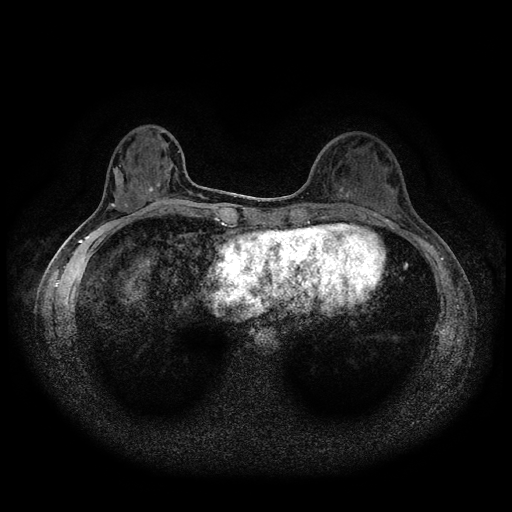
Breast MRI (dynamic contrast-enhanced, multi-phase), one axial slice. Position 34 of 116 along the scan axis. Dynamic contrast-enhanced series, time point 2 of 5 at this slice position (early post-contrast). 1.5 T. TE 2.7 ms, TR 5.4 ms. 2 mm slice thickness. 512 × 512 image matrix, field of view 330 × 330 mm. Female patient, age 36 years.
Outlined on this slice (semi-automatically segmented with operator editing):
- breast lesion (labelled benign in the annotation): box from (x=335, y=178) to (x=358, y=204) px